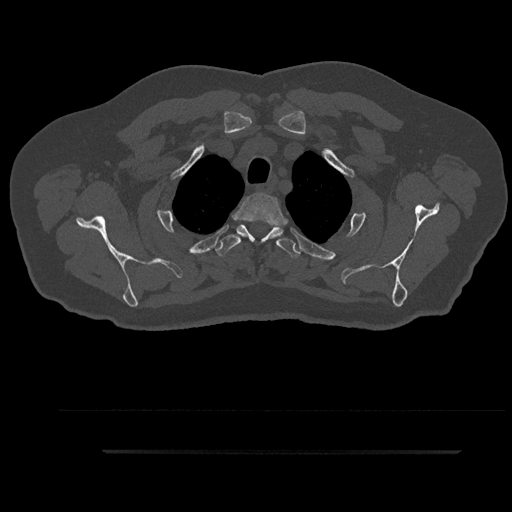
CT including the spine, one axial slice. Slice 738 of 797 in the series (ordered by position). Reconstruction kernel Br40s/3. 120 kVp. Bone window (W 1800 / L 400 HU). 0.5 mm slice thickness. 512 × 512 image matrix. Patient: male, 63 years. From the clinical record (not read from this slice): primary cancer: renal; vertebrae with lytic lesions (as recorded): T8.
Outlined on this slice (semi-automatic segmentation, software-assisted and operator-edited):
- T2 vertebra: box from (x=236, y=192) to (x=284, y=244) px
- T3 vertebra: (x=215, y=224)–(x=301, y=258)